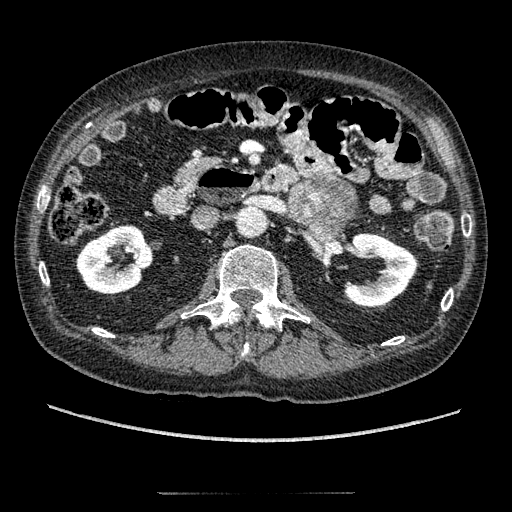
Contrast-enhanced abdominal CT, one axial slice. Position 90 of 274 along the scan axis. Reconstruction kernel STANDARD. Intravenous contrast given. Soft-tissue window (W 400 / L 40 HU). 512 × 512 image matrix, field of view 381 × 381 mm. Patient: male, 69 years. From the clinical record (not read from this slice): diagnosis: adrenocortical carcinoma; tumour side: left adrenal; tumour size at pathology: 6.1 cm; Ki-67 index: 10 %; stage (as recorded): 3.
Annotated regions visible in this slice (semi-automatic segmentation, software-assisted and operator-edited):
- mass: bounding box <289,181,355,236> (left, top, right, bottom; pixels)